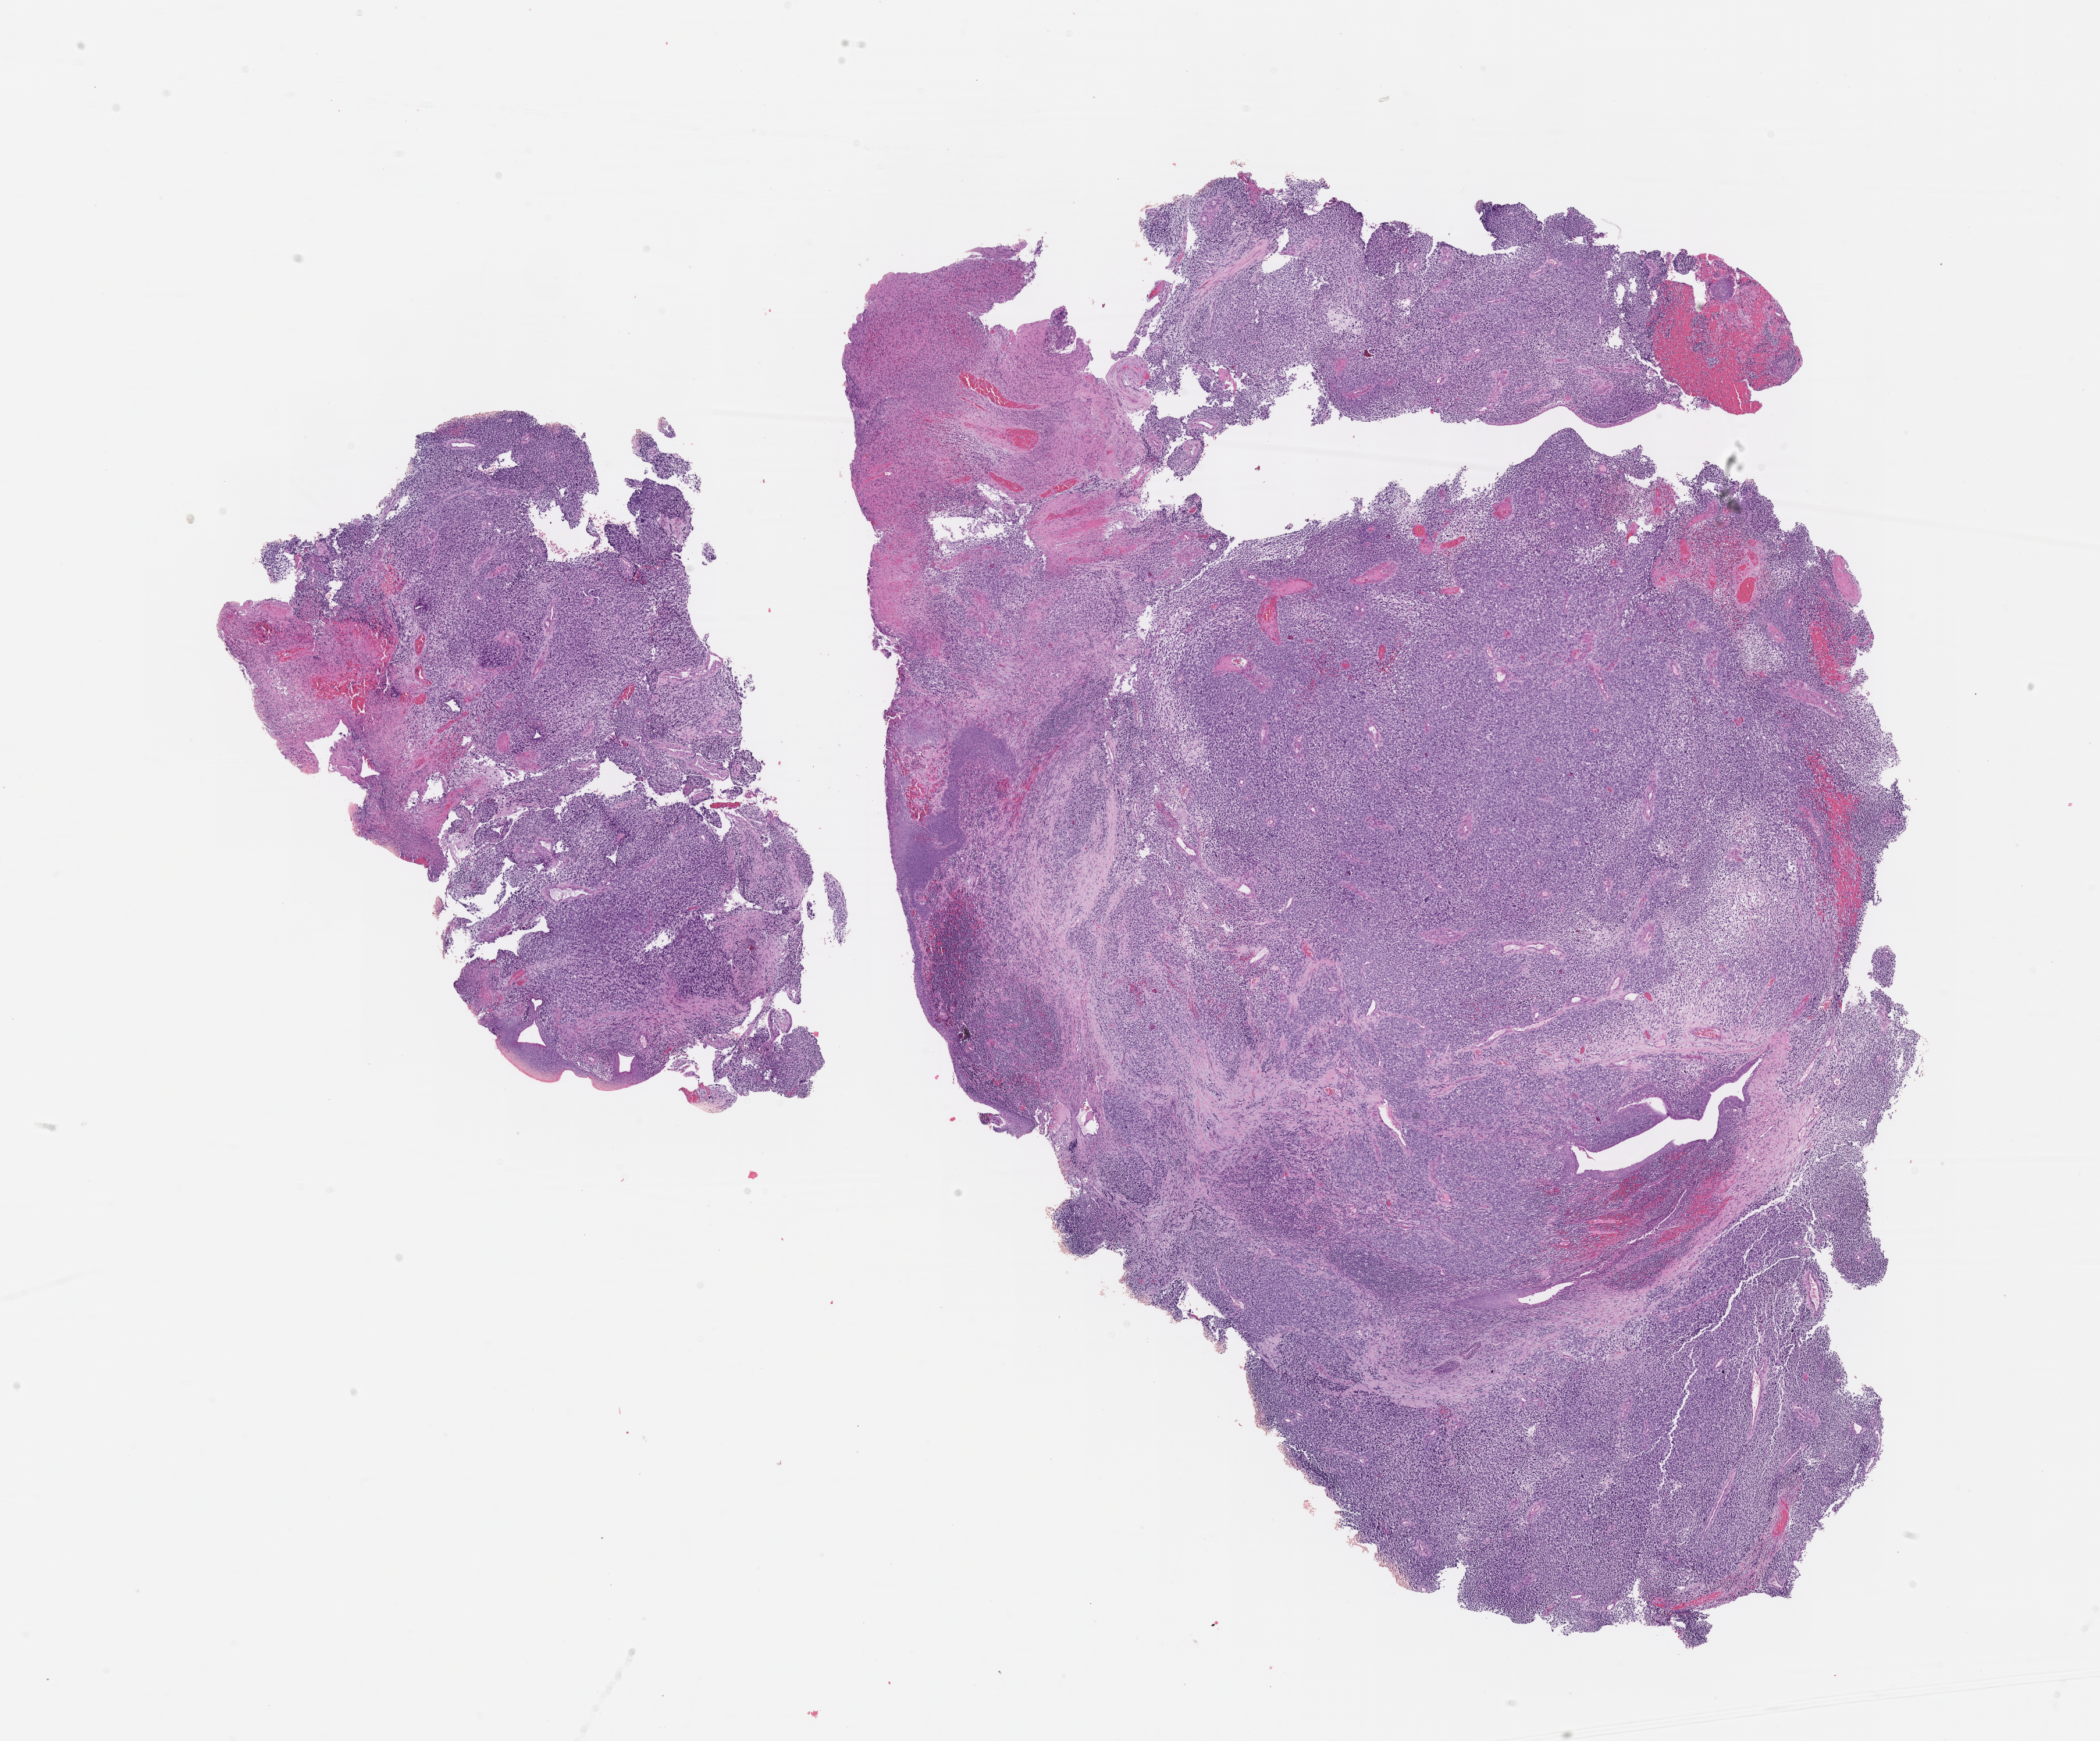
Digitized haematoxylin and eosin-stained section of tumor tissue — a low-resolution overview of the entire scanned area, about 14.6 x 12.1 mm, formalin-fixed paraffin-embedded section, sample anatomic site: nasopharynx-left. Patient: male, age 5.2 years at diagnosis.
Diagnosis: rhabdomyosarcoma; histological classification: embryonal rhabdomyosarcoma. Stage (as recorded): 3. Primary site (case record): nasopharynx (PM). Metastatic status at presentation (as recorded): non-metastatic (confirmed).